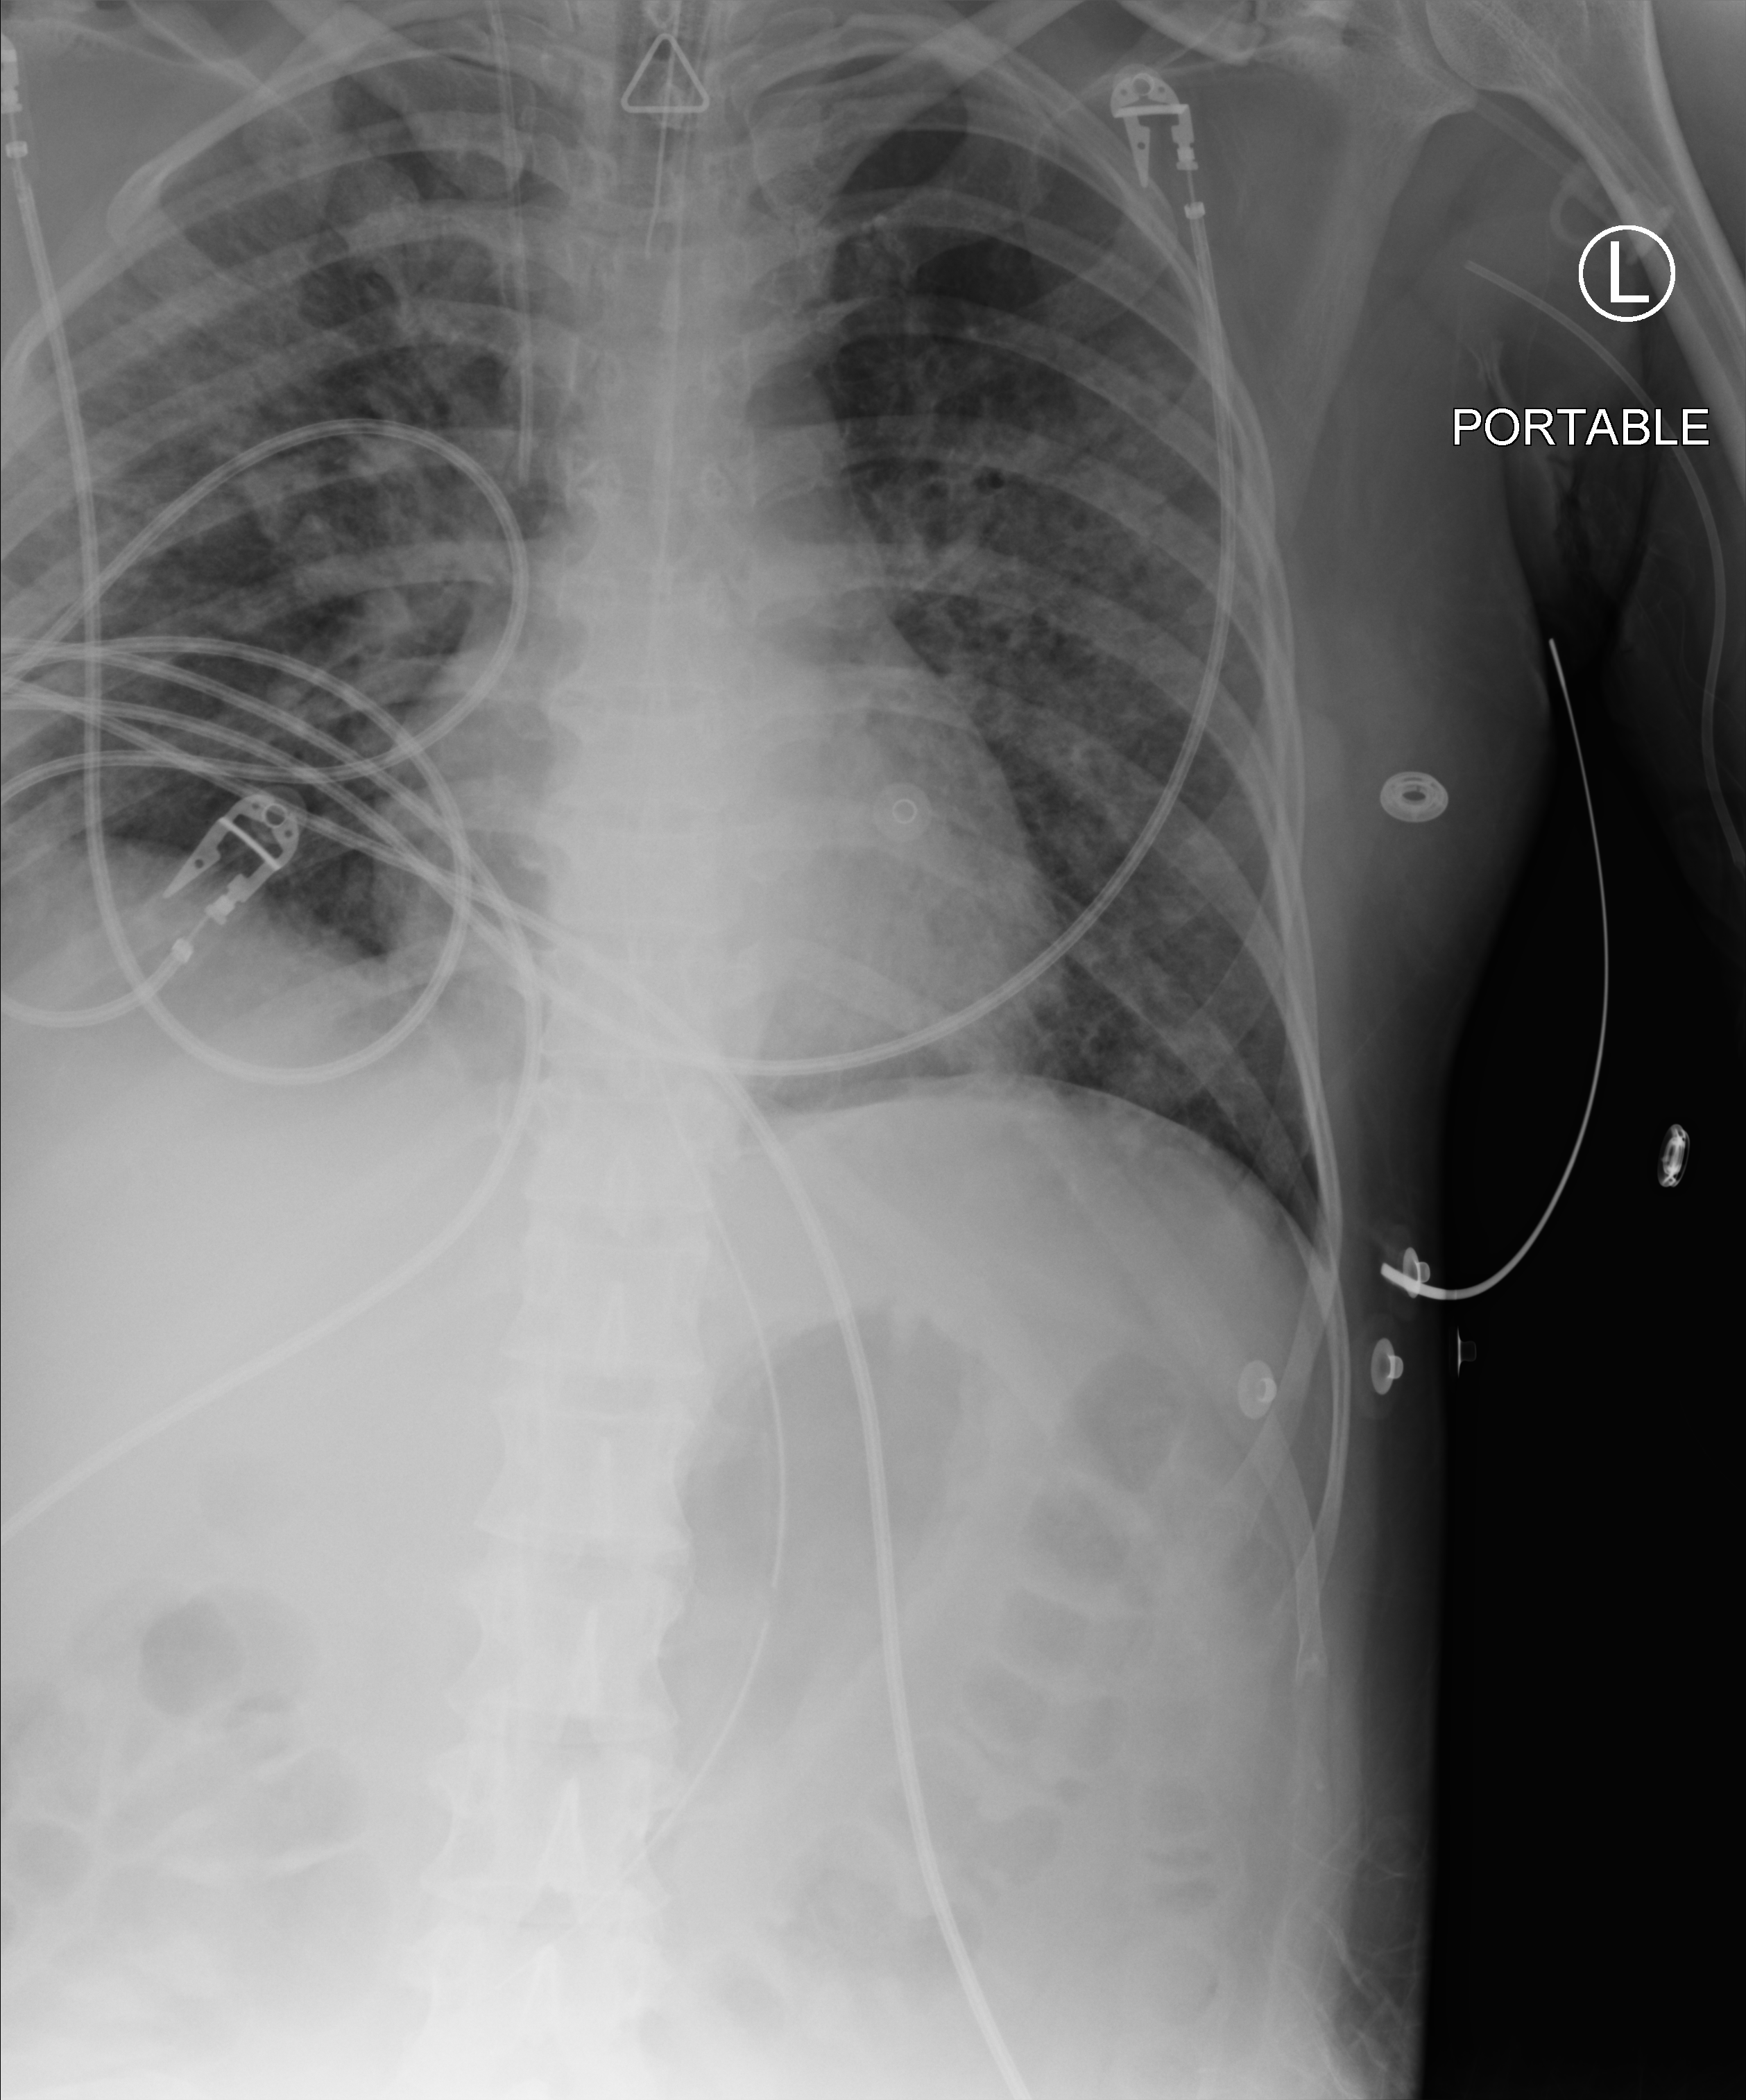
Bedside chest radiograph (computed radiography), anteroposterior (AP) projection. Female patient hospitalised with COVID-19, age 18–59 years.
Hospital-stay facts (about this admission, not read from this image; timing relative to this image not recorded):
- mechanically ventilated during this hospital stay: yes
- length of hospital stay: 71 days
- COPD (admission record): no